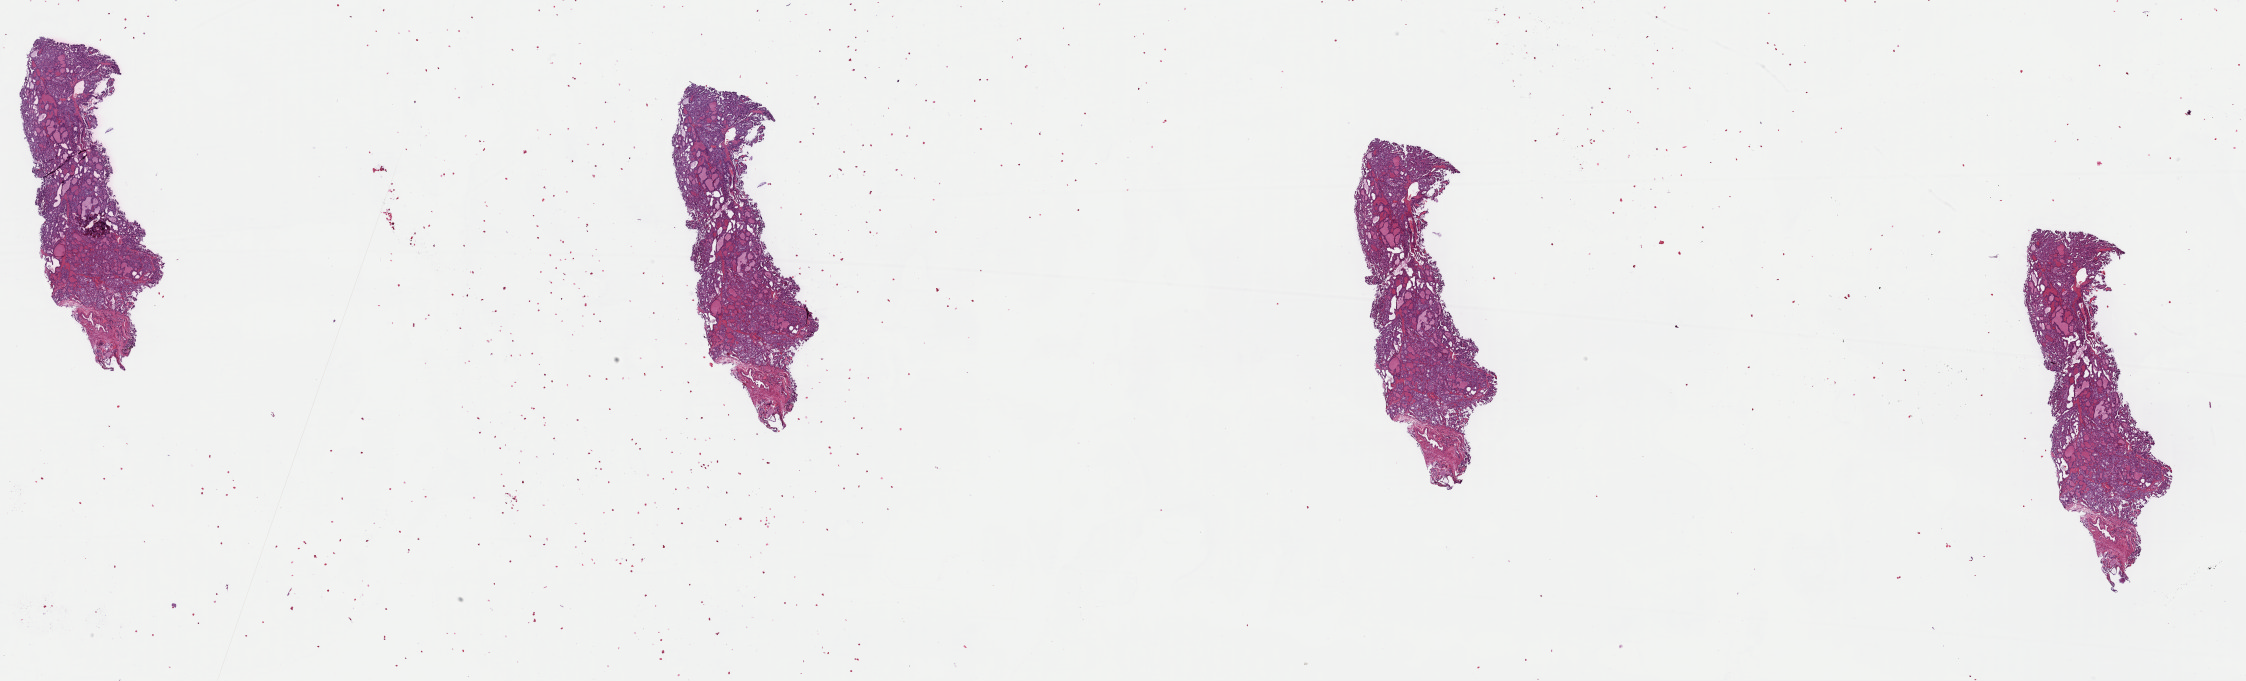
Hematoxylin and eosin (H&E) stained whole-slide image — low-resolution overview of the scanned area, about 35.5 x 10.8 mm (acquisition: 40x scan). FFPE section. Primary tumour sample from the thyroid. Patient: female, age at initial diagnosis 41 years.
Diagnosis: Papillary carcinoma, follicular variant (thyroid gland).